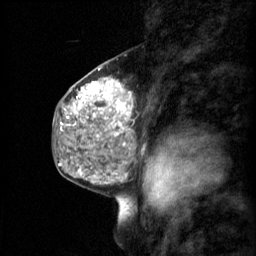
Breast MRI (dynamic contrast-enhanced), one sagittal slice; position 33 of 60 along the scan axis; 3 images stored at this slice position (order not interpretable as contrast timing); 1.5 T; TE 4.2 ms, TR 11 ms; 256 × 256 image matrix, field of view 200 × 200 mm. Female patient, age 48 years.
Structures marked on this image (semi-automatically segmented with operator editing):
- analysis volume of interest (the breast-tissue region the enhancement analysis was run in; not a lesion): bounding box [x1, y1, x2, y2] px = [69, 74, 134, 147]
- tumour enhancement mask (voxels above the 70 % enhancement threshold inside the analysis volume of interest): [77, 78, 134, 147]